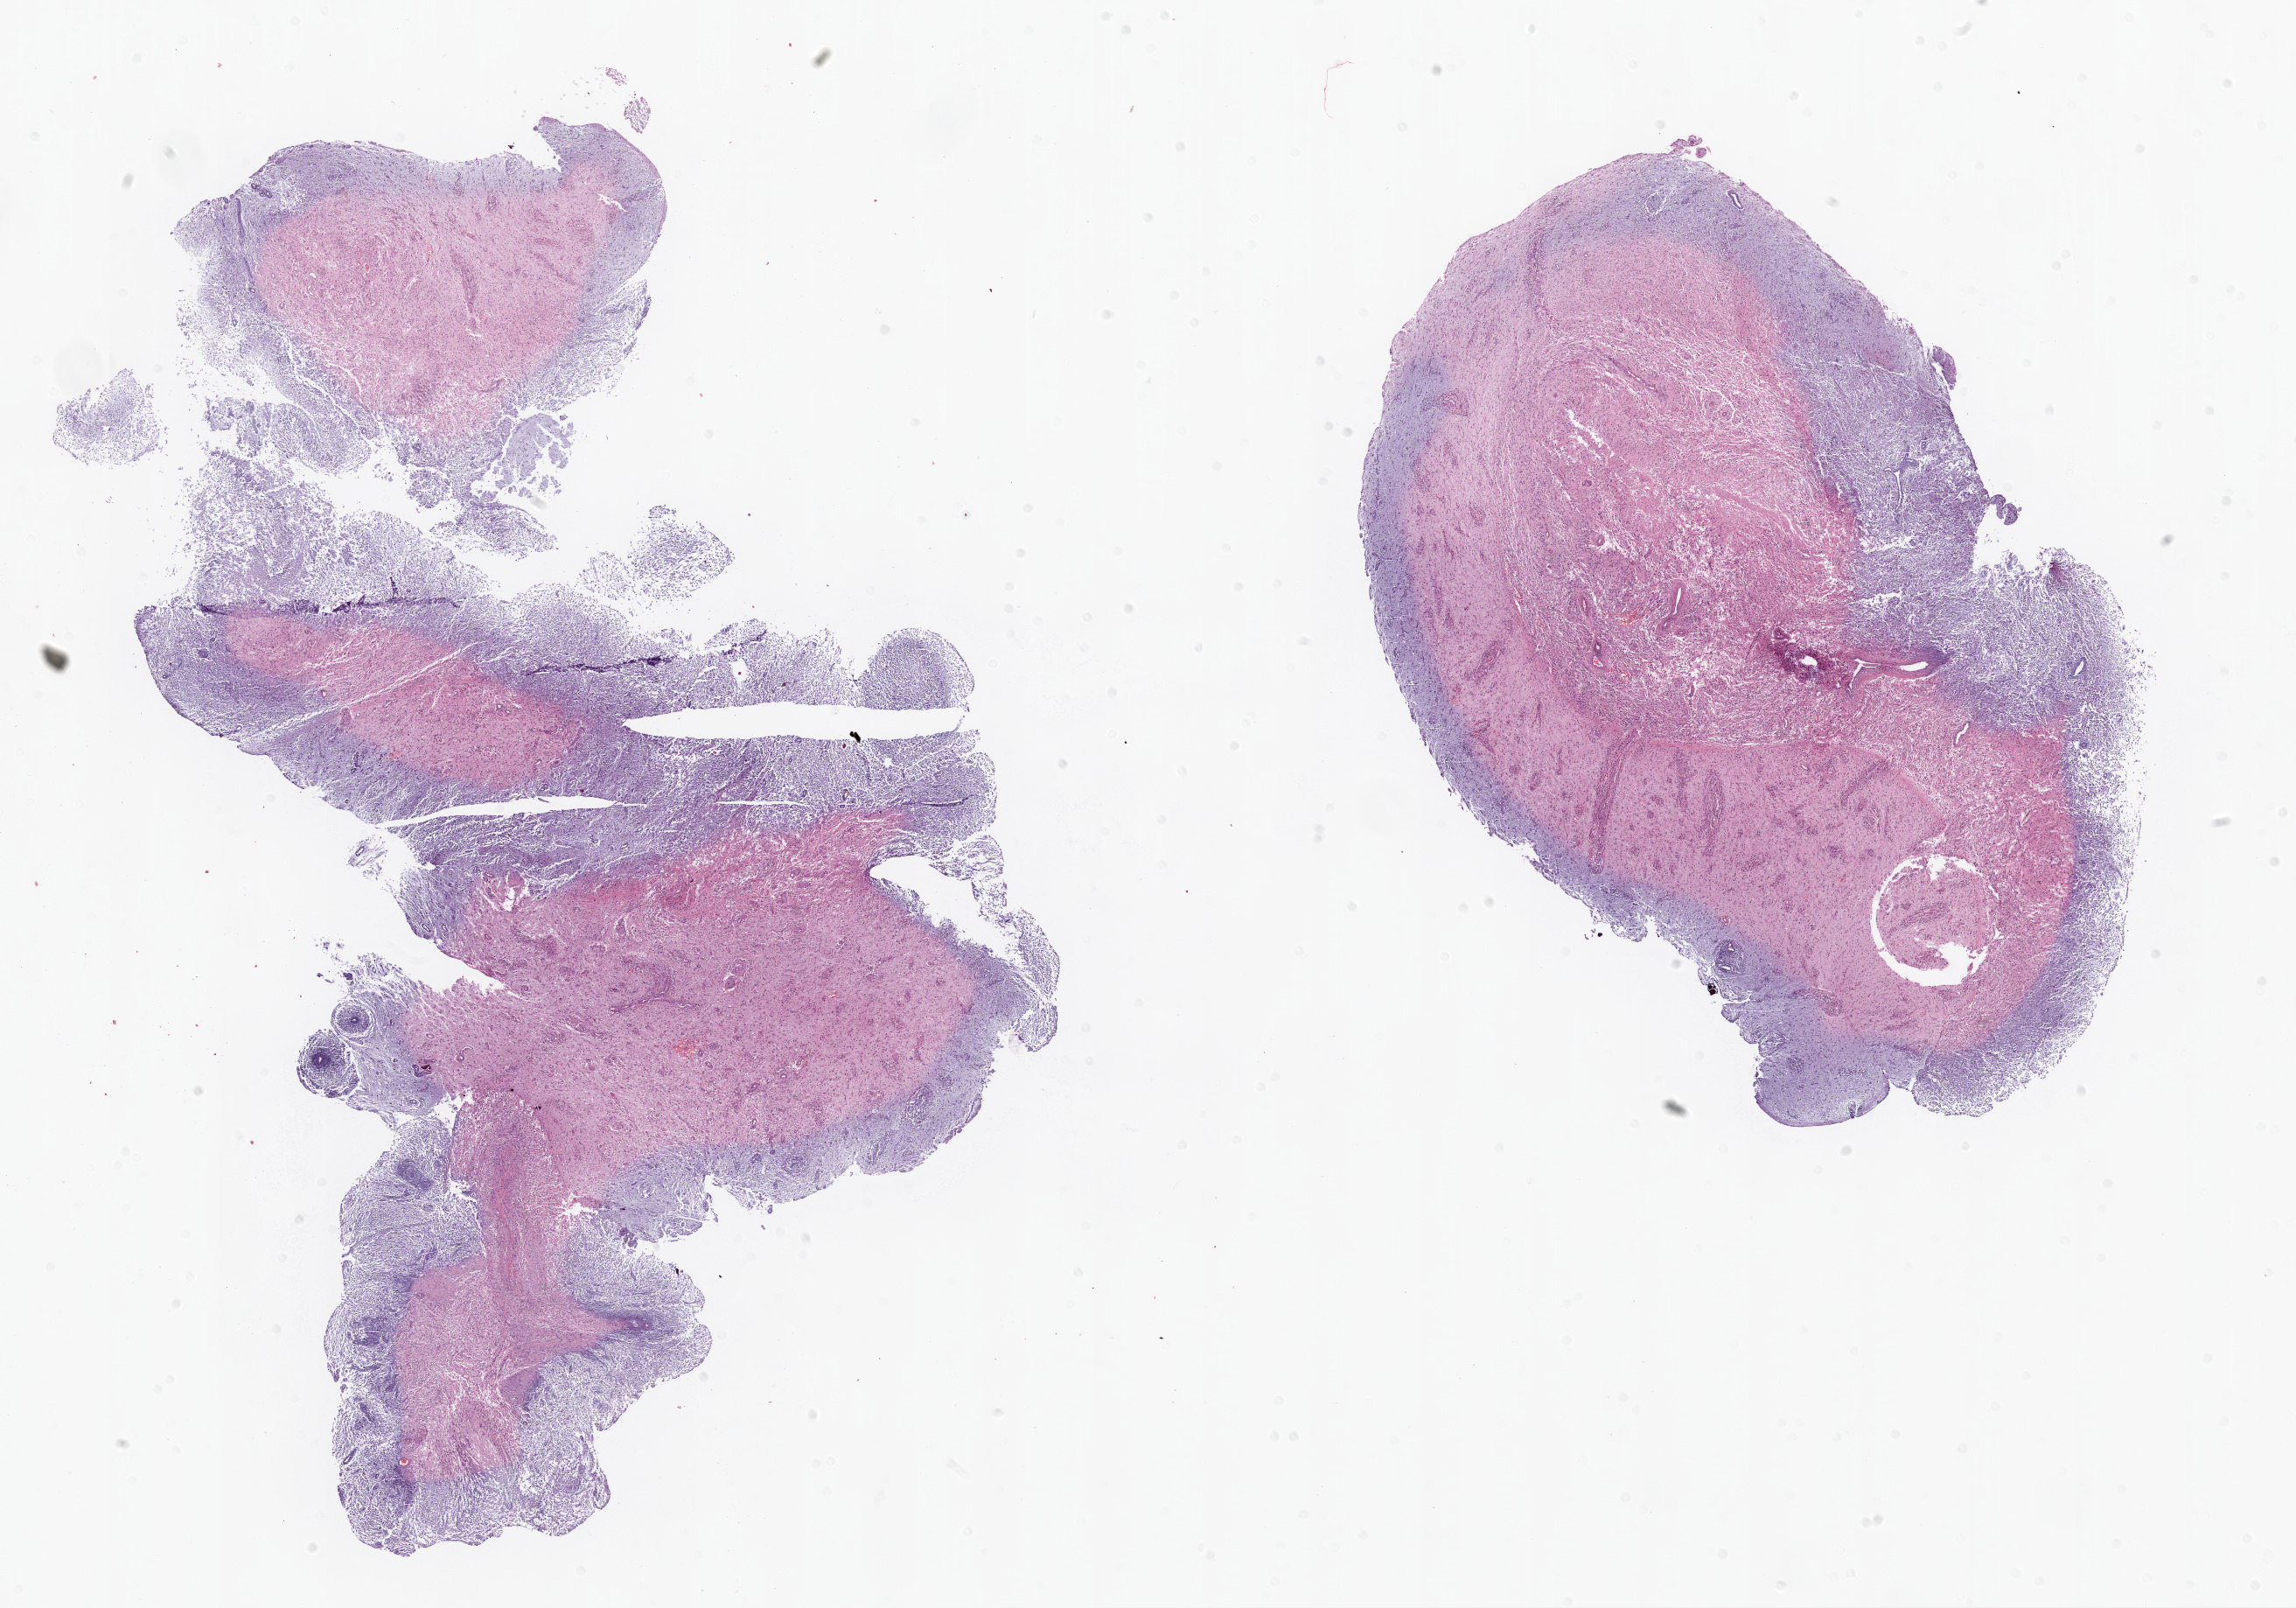
H&E-stained whole-slide image — whole scanned area (about 21.1 x 14.7 mm, slide scanned at 20x) shown as a low-resolution overview, FFPE section, sample: primary tumour, brain. Patient: female, age at initial diagnosis 82 years.
• histologic diagnosis: Glioblastoma